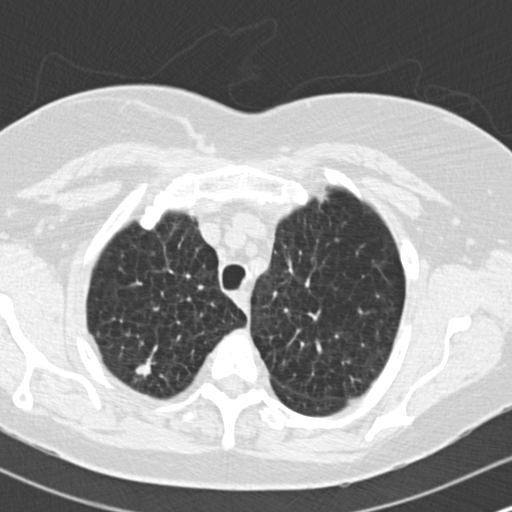
Axial slice from a low-dose chest CT screening exam; first (baseline) screen; lung window (W 1500 / L -600 HU); 2 mm slice thickness; 120 kVp; slice 30 of 172 in the series; 512 × 512 image matrix, field of view 310 × 310 mm. Female participant, aged 73 years at enrolment. Former smoker at enrolment.
Expert reader's lesion annotation, bounding box (x1, y1, x2, y2) in pixels: (120, 338, 173, 388). The screening reader recorded 2 non-calcified nodules or masses ≥4 mm on this exam (right upper lobe, right upper lobe); which of them this box marks is not recorded. Participant outcome: lung cancer diagnosed 601 days after this screen — adenocarcinoma, NOS, right upper lobe, moderately differentiated (G2), stage IB (AJCC 6th edition), 15 mm at pathology.